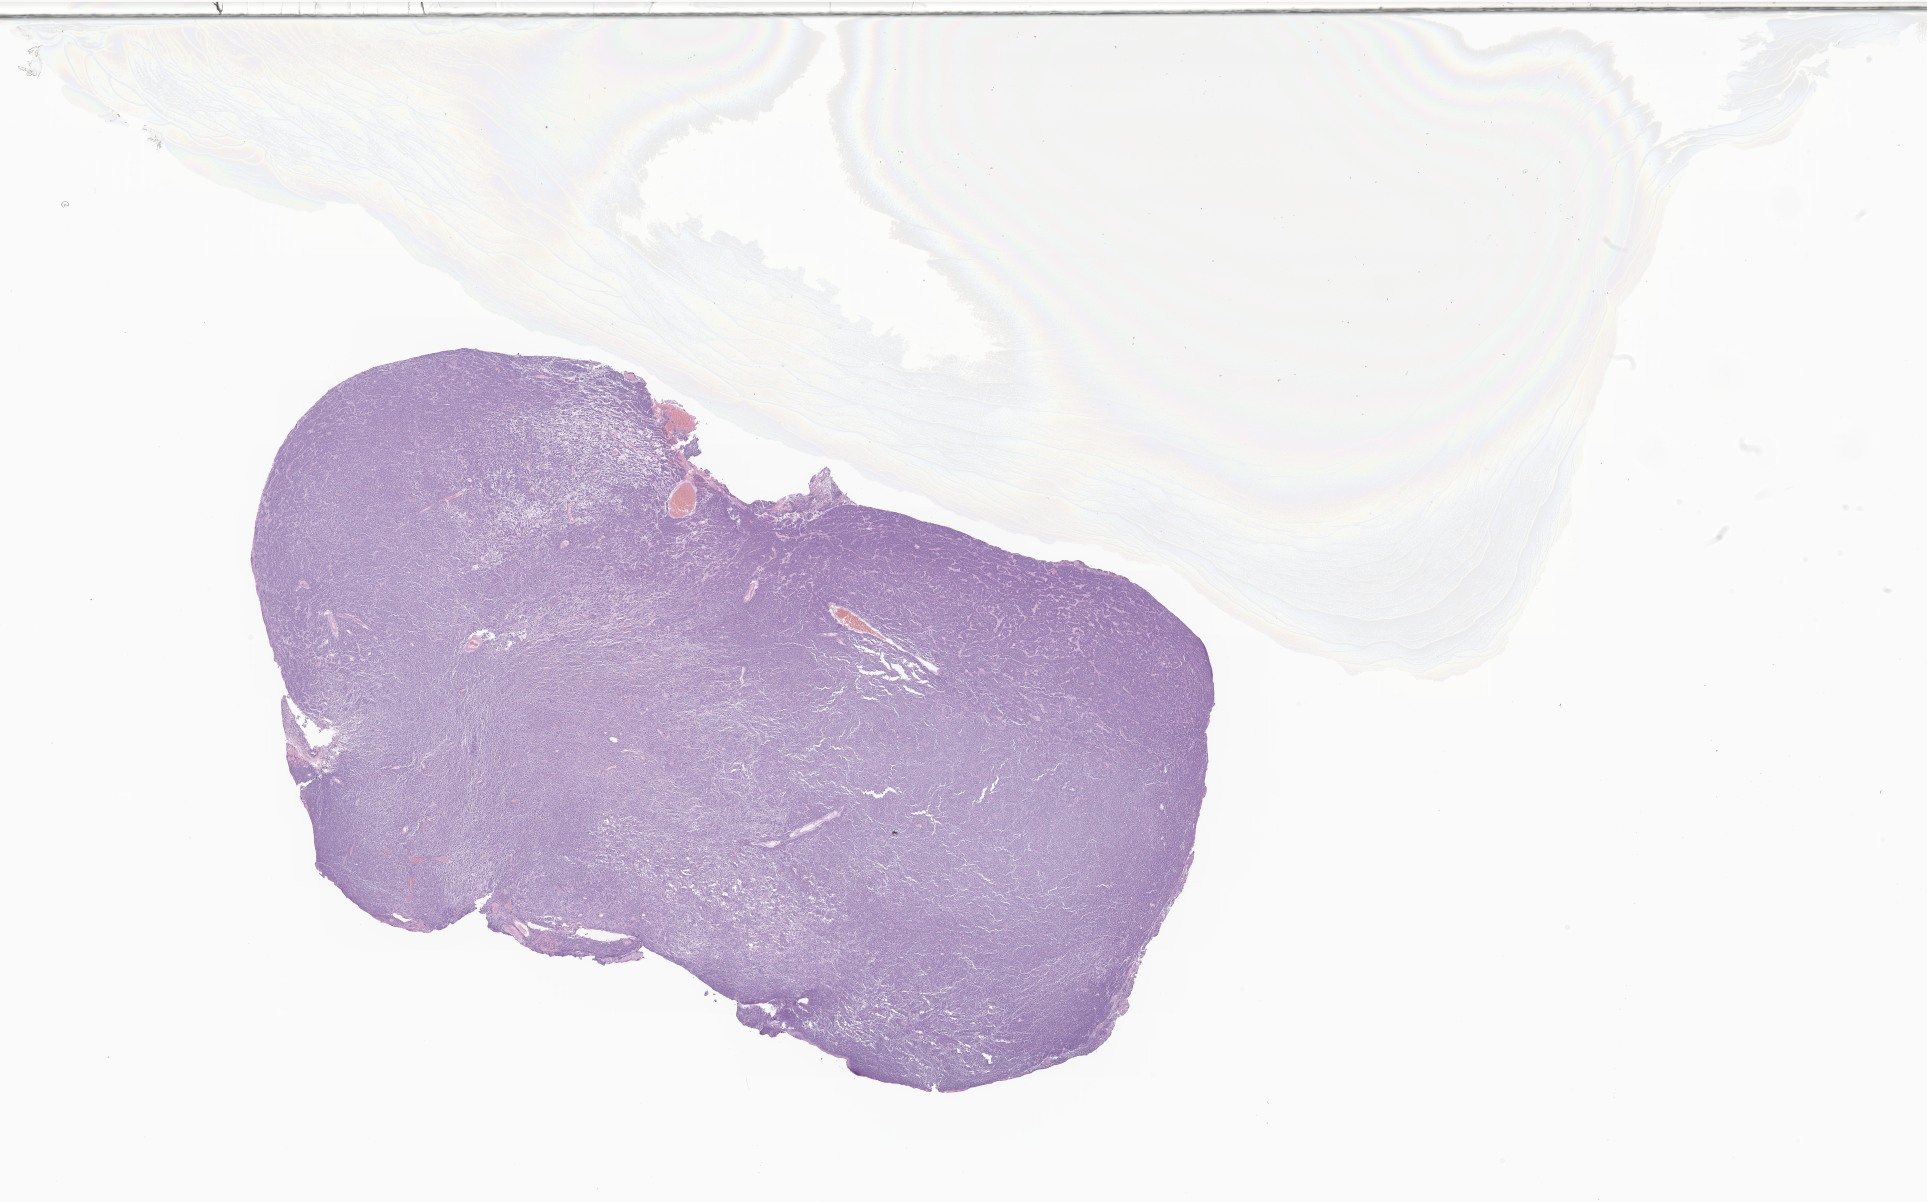
Digitized hematoxylin and eosin (H&E)-stained section of tumor tissue from the brain — shown as a low-resolution overview of the whole scanned area (about 32.5 x 20.3 mm), formalin-fixed paraffin-embedded section. Patient: female, age 167 months (13 years 11 months).
Diagnosis (ICD-O-3 morphology term): Medulloblastoma, NOS.